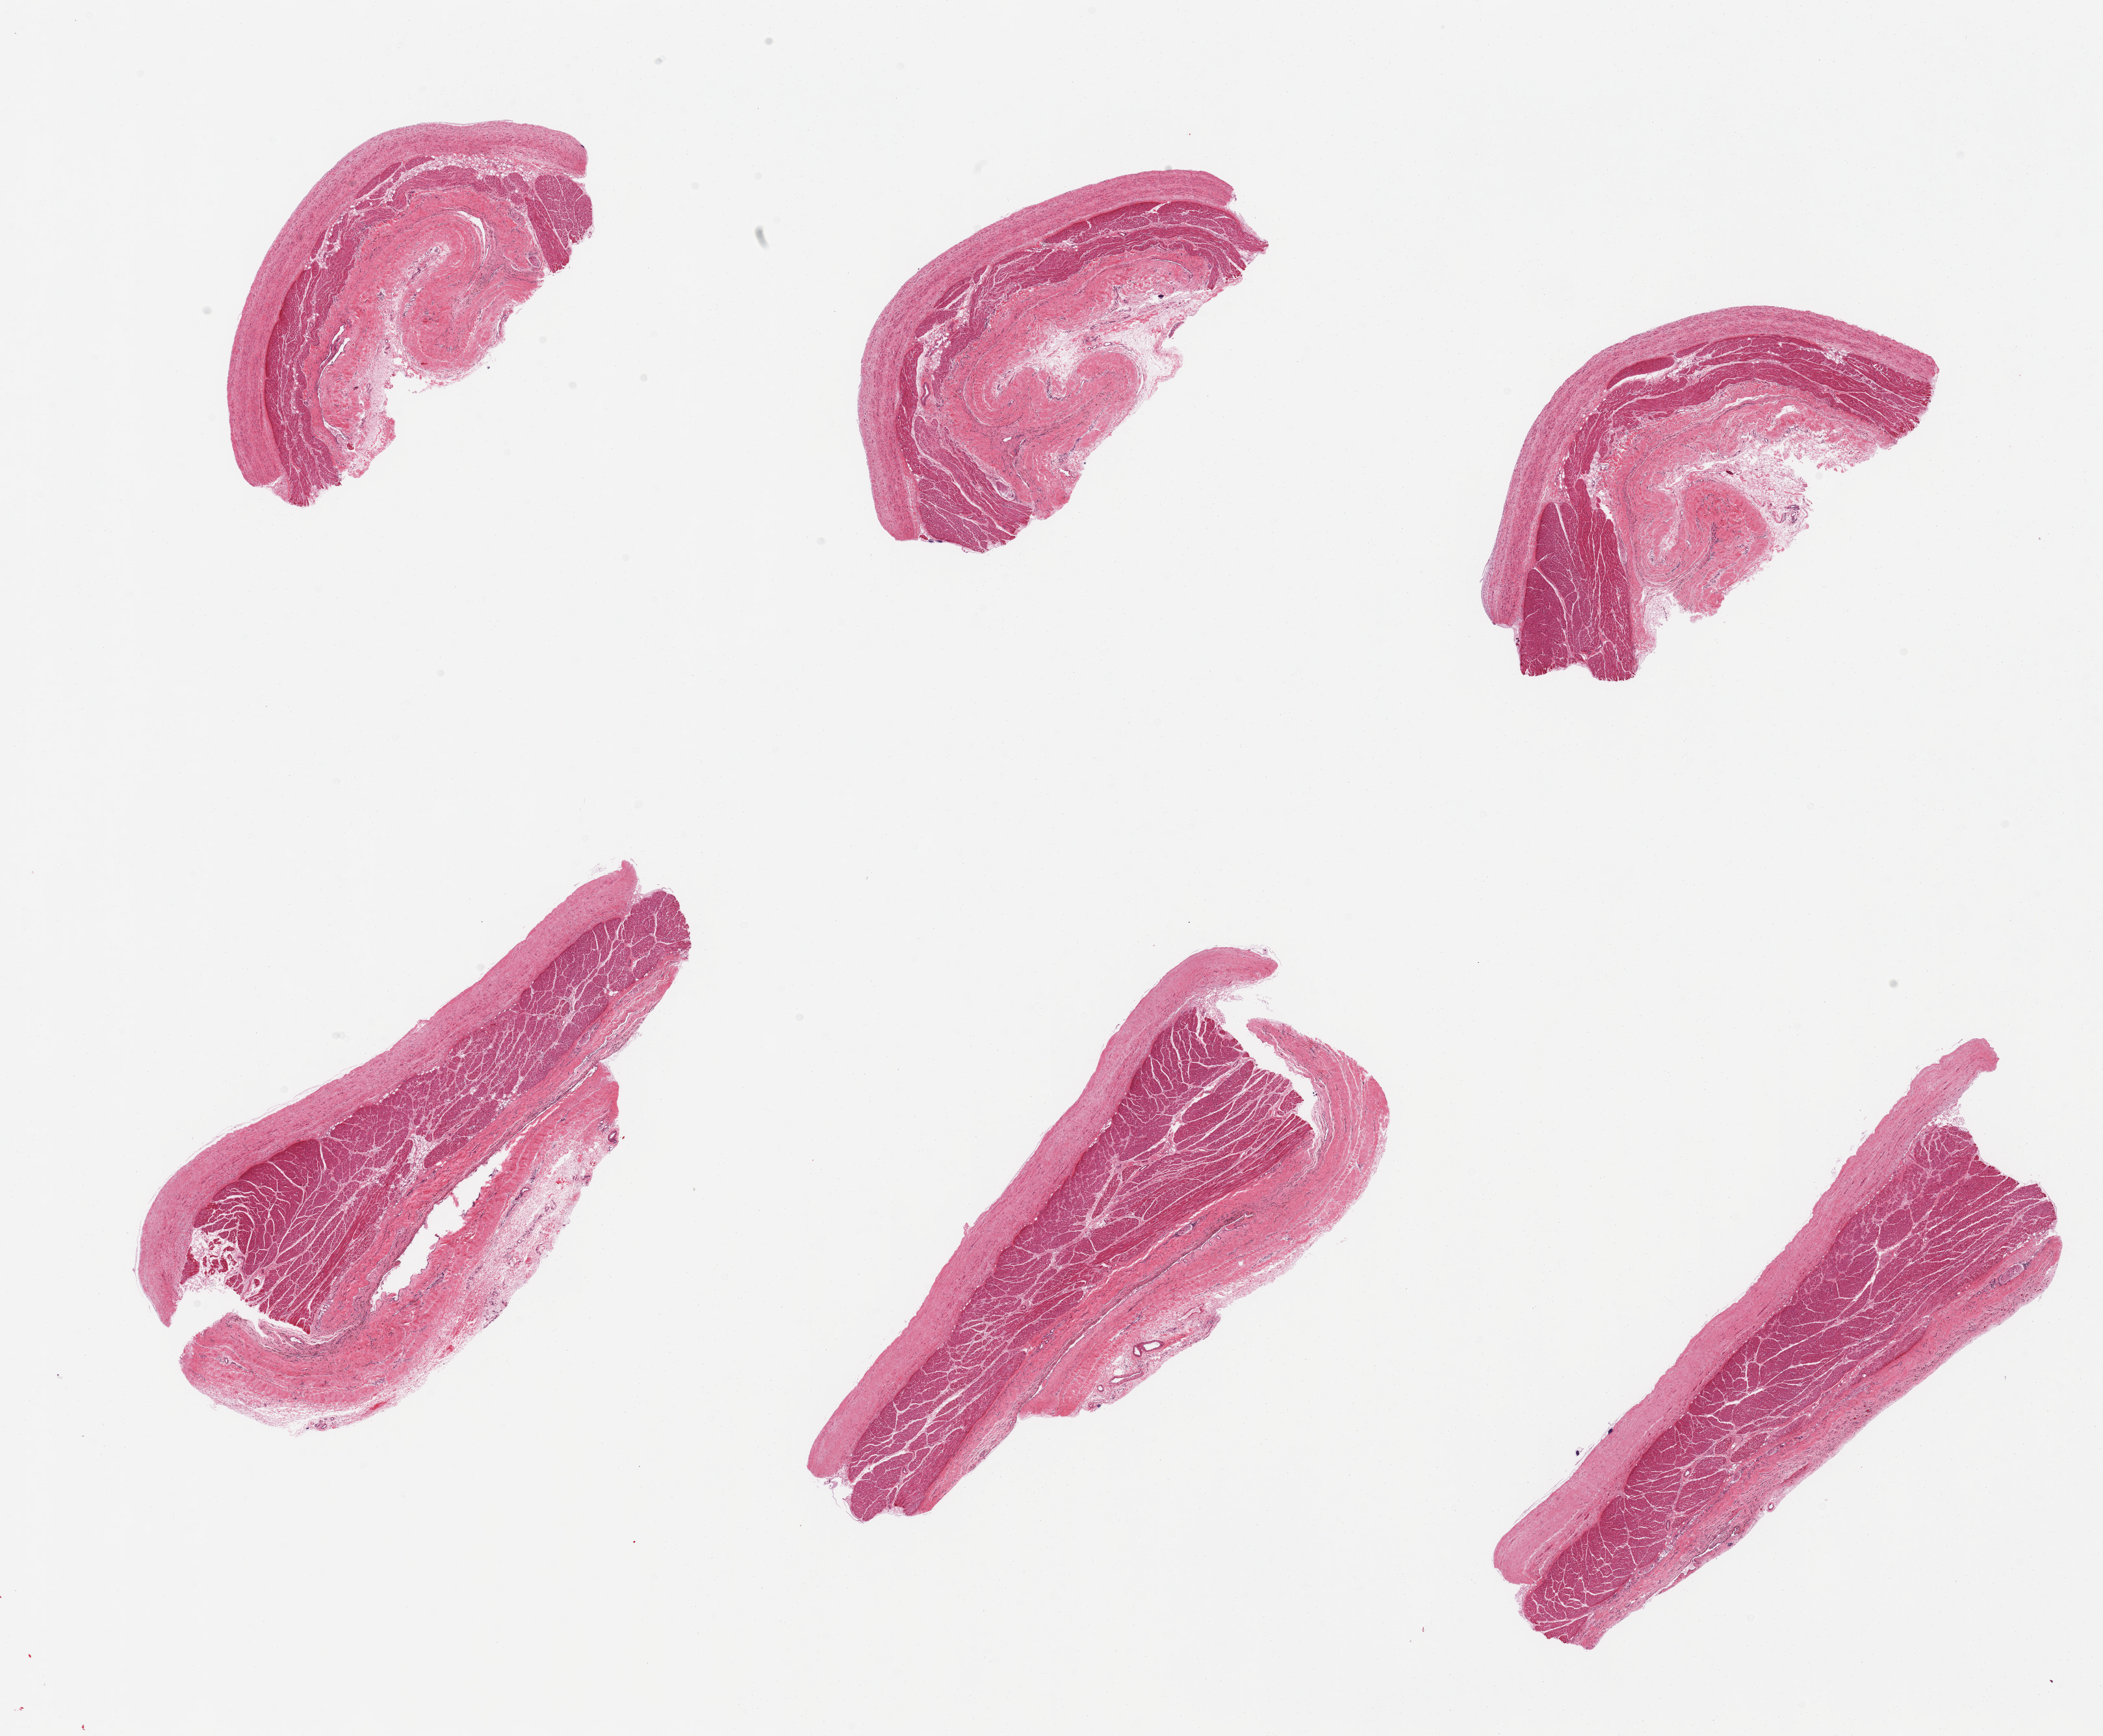
Haematoxylin and eosin whole-slide image — a low-resolution overview of the entire scanned area, about 25.6 x 21.1 mm. PAXgene-fixed, paraffin-embedded tissue. Section of auricular appendage (target tissue). Donor tissue sample. Donor: male.
Review note (as recorded): 6 pieces; thick (up to 0.5 mm) fibrous layers 50% of area.